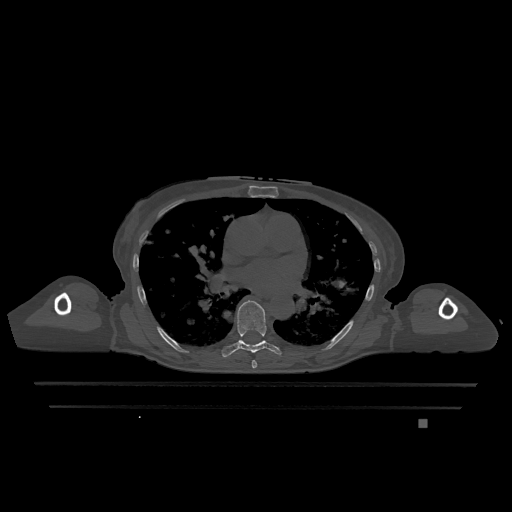
CT including the spine, one axial slice; position 741 of 1317 along the scan axis; bone window (W 1800 / L 400 HU); 0.5 mm slice thickness; 512 × 512 image matrix. Patient: female, 74 years. Case-level facts recorded for this patient, not image findings: primary cancer: lung; vertebrae with lytic lesions (as recorded): T1, T4, T5, T6, L4, L5.
Outlined on this slice (semi-automatically segmented with operator editing):
- T6 vertebra: bounding box [x1, y1, x2, y2] px = [252, 360, 257, 369]
- T7 vertebra: [222, 300, 282, 358]